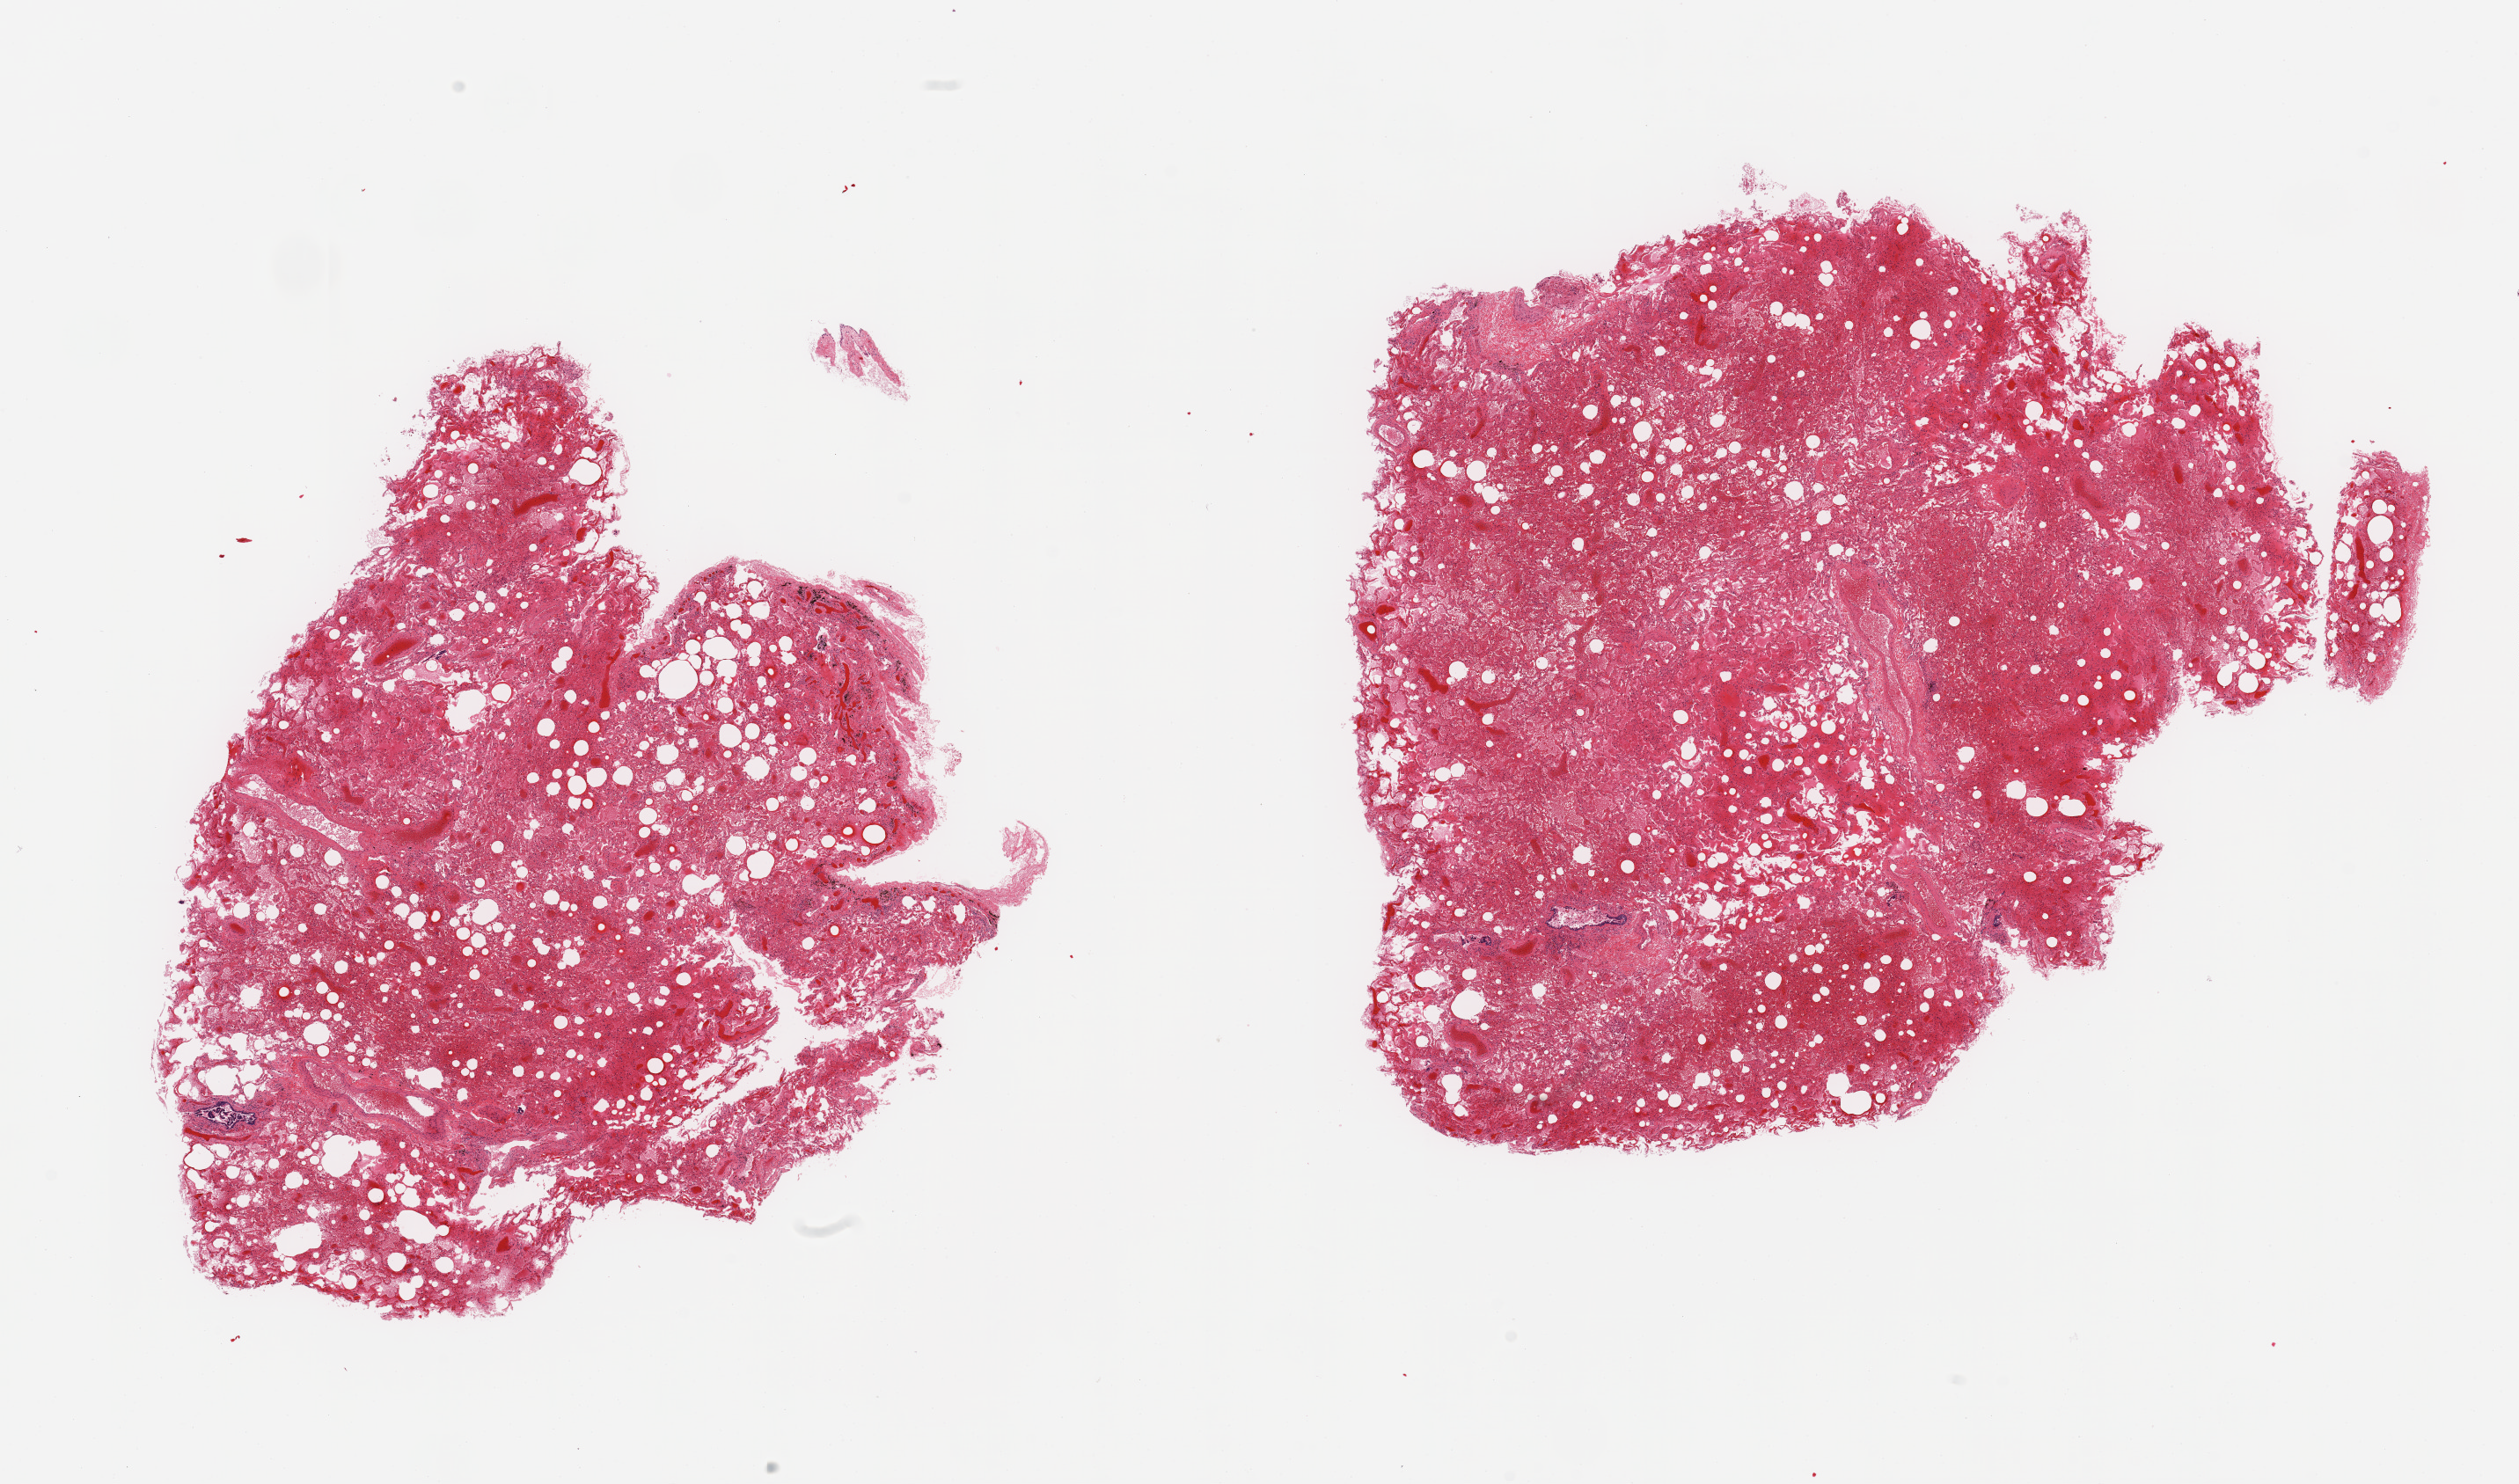
Whole-slide image, H&E stain — low-resolution overview of the scanned area, about 22.6 x 13.3 mm, PAXgene-fixed paraffin-embedded (PFPE) section, sampled site (target tissue): lung, donor tissue sample. Donor sex: male.
Review note (as recorded): 2 pieces; severe congestion and intraalveolar hemorrhage, focal pleural coverage with fibrosis and anthracotic pigmentation, a few small bronchi with sloughed mucosa.